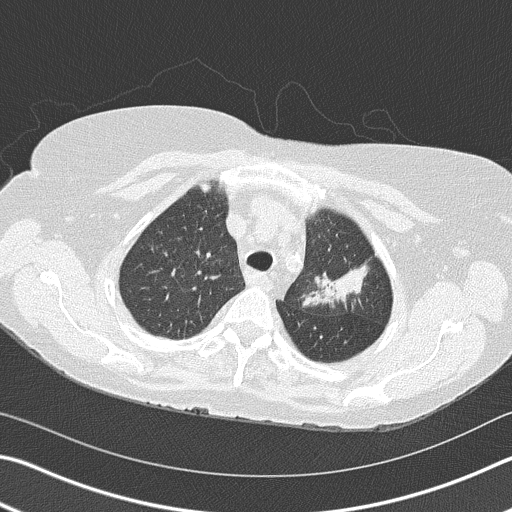
Chest CT (low-dose screening protocol), one axial image, second annual screen, lung window (W 1500 / L -600 HU), 2 mm slice thickness, lung (sharp) reconstruction kernel (B50f). Female, age 68 years at enrolment. Former smoker at enrolment.
• Expert reader's lesion annotation, bounding box [x1, y1, x2, y2] px = [291, 226, 378, 322].
• The exam's reader record, not a measurement of the box and not confirmed to be the same lesion: non-calcified nodule or mass ≥4 mm, left upper lobe, 4 × 2 mm, spiculated (stellate) margins, soft tissue attenuation, pre-existing on the prior screen: yes; interval growth: yes.
• Lung cancer was diagnosed 392 days after this screen: adenocarcinoma, NOS, left upper lobe, poorly differentiated (G3), stage IB (AJCC 6th edition), 50 mm at pathology.